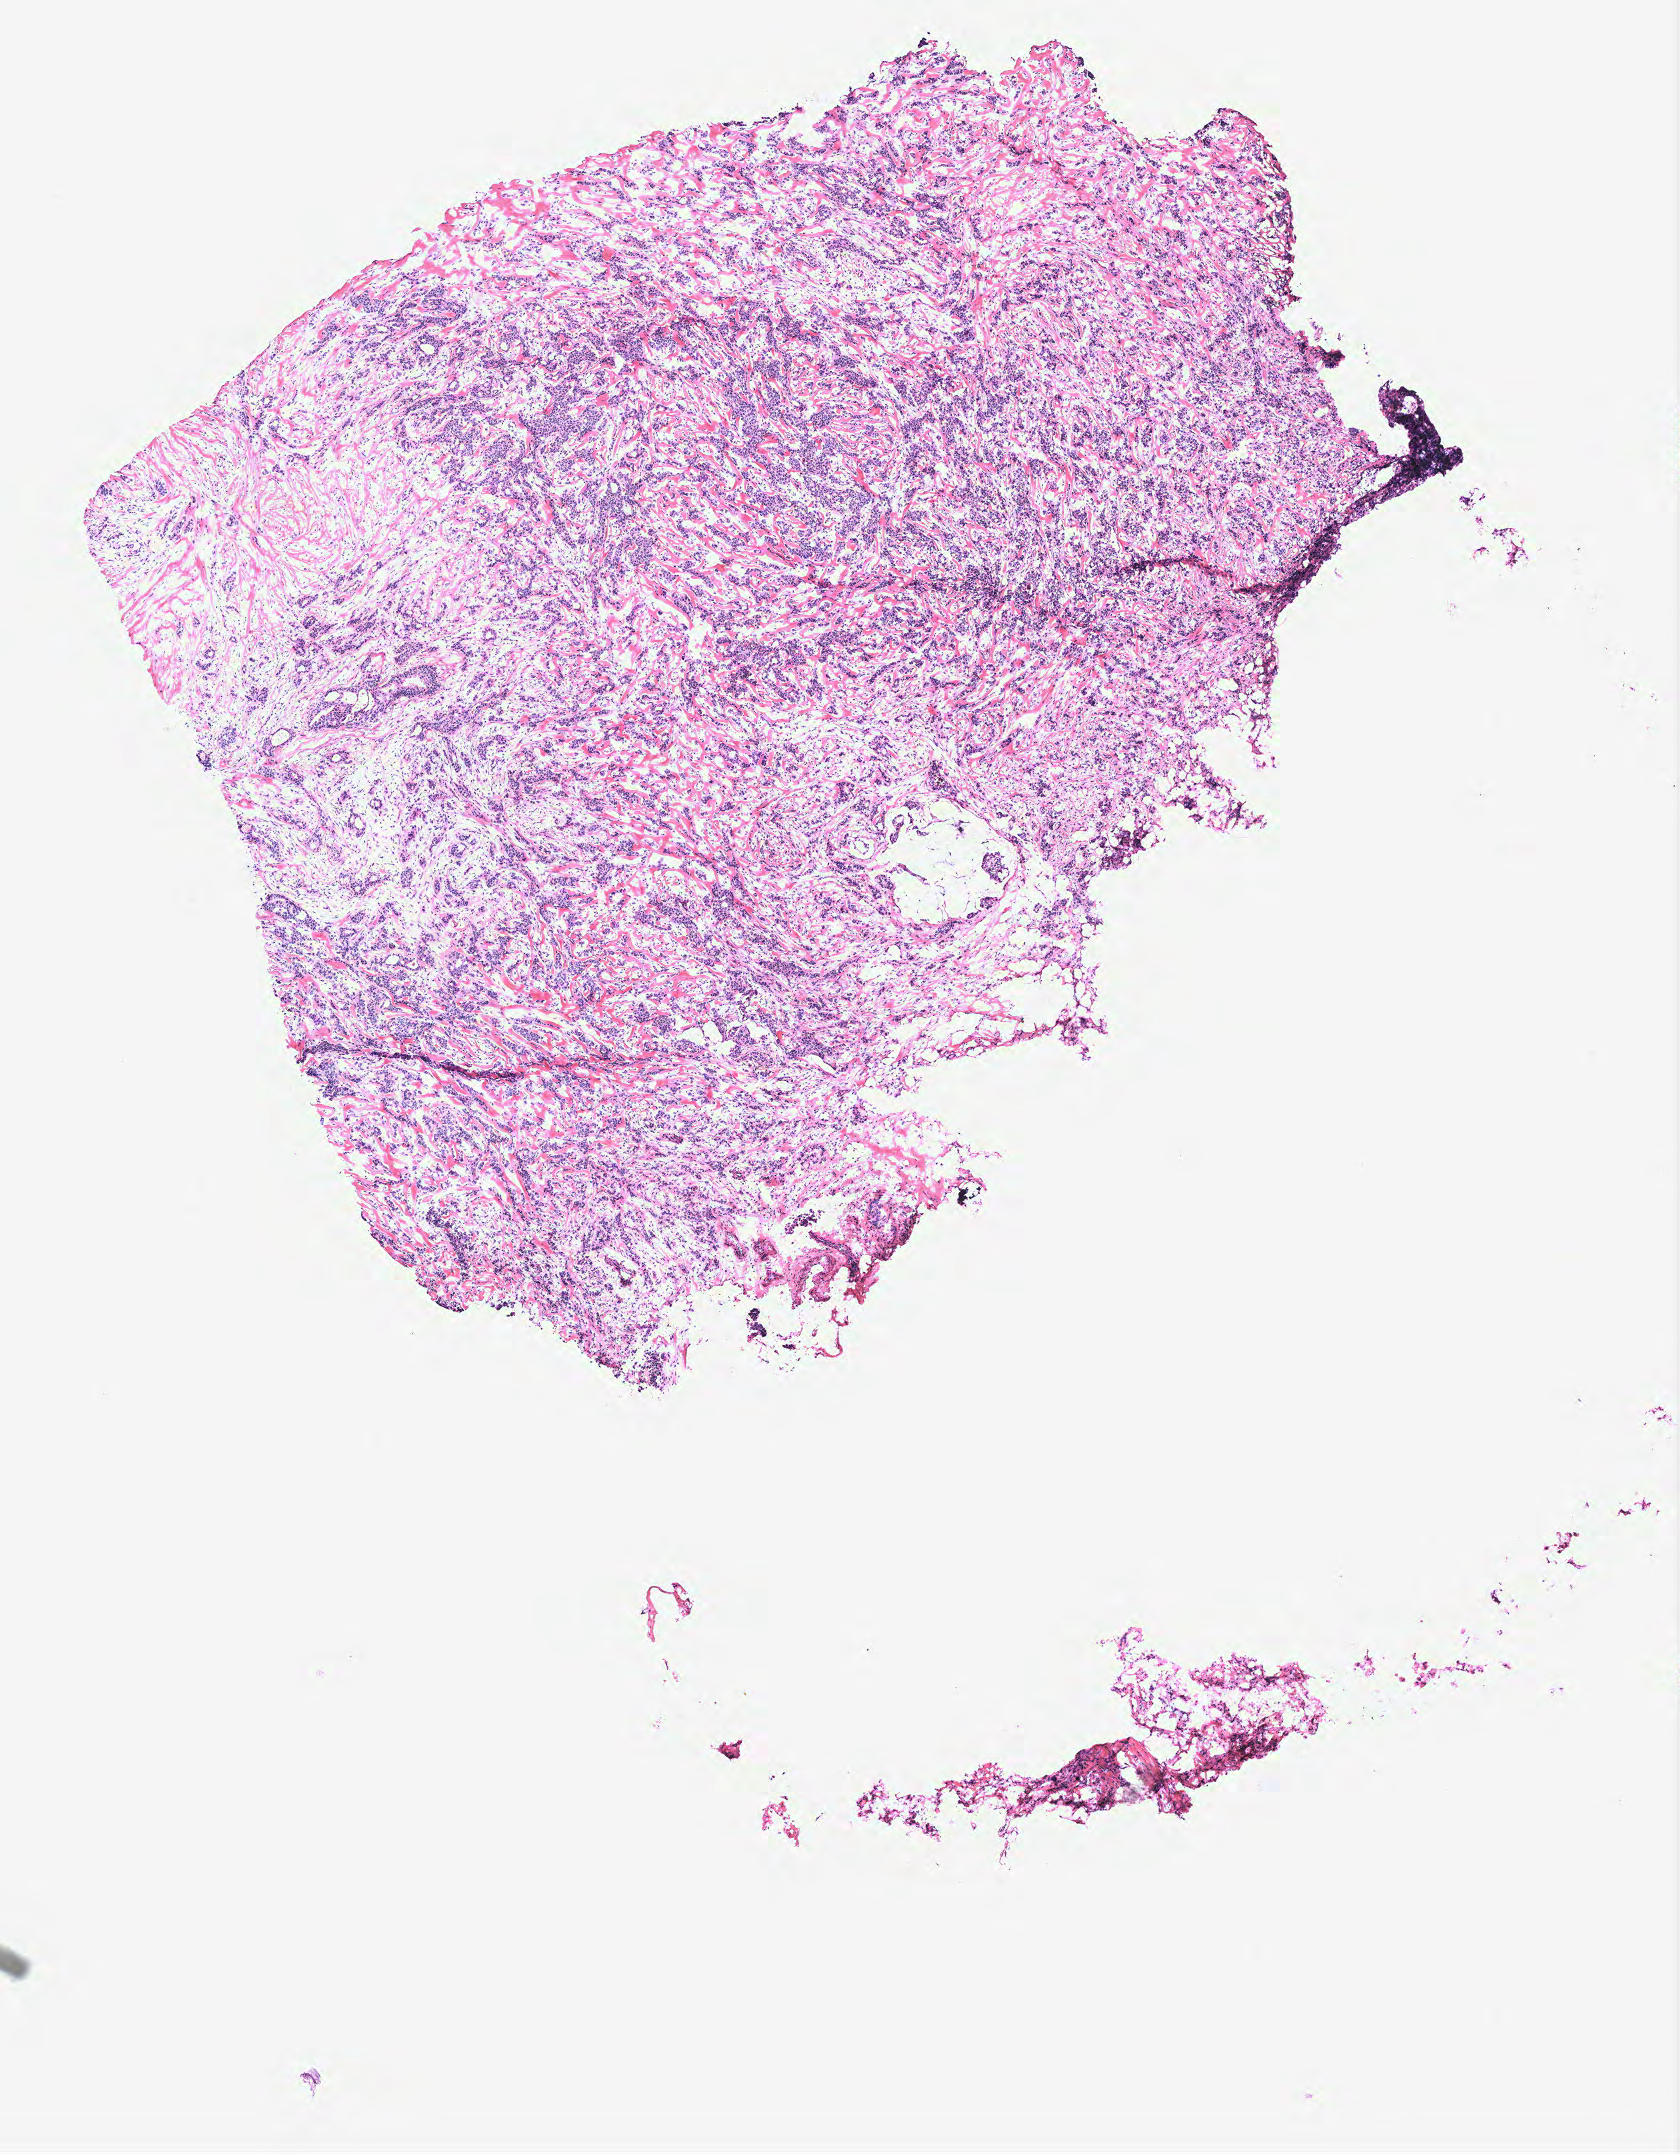
Hematoxylin and eosin (H&E) stained whole-slide image, a low-resolution overview of the entire scanned area, about 6.7 x 8.6 mm; breast, tissue type not recorded.
Patient diagnosis (cohort enrolment): breast cancer (breast).